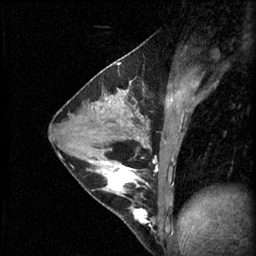
Breast MRI (dynamic contrast-enhanced), one sagittal slice. Position 31 of 60 along the scan axis. 3 images stored at this slice position (order not interpretable as contrast timing). 1.5 T. TE 4.2 ms, TR 11 ms. 2.1 mm slice thickness. 256 × 256 image matrix. Female patient, age 29 years.
Annotated regions visible in this slice (semi-automatic segmentation, software-assisted and operator-edited):
- analysis volume of interest (the breast-tissue region the enhancement analysis was run in; not a lesion): bounding box (x1, y1, x2, y2) in pixels: (93, 164, 149, 229)
- tumour enhancement mask (voxels above the 70 % enhancement threshold inside the analysis volume of interest): (97, 166, 149, 223)